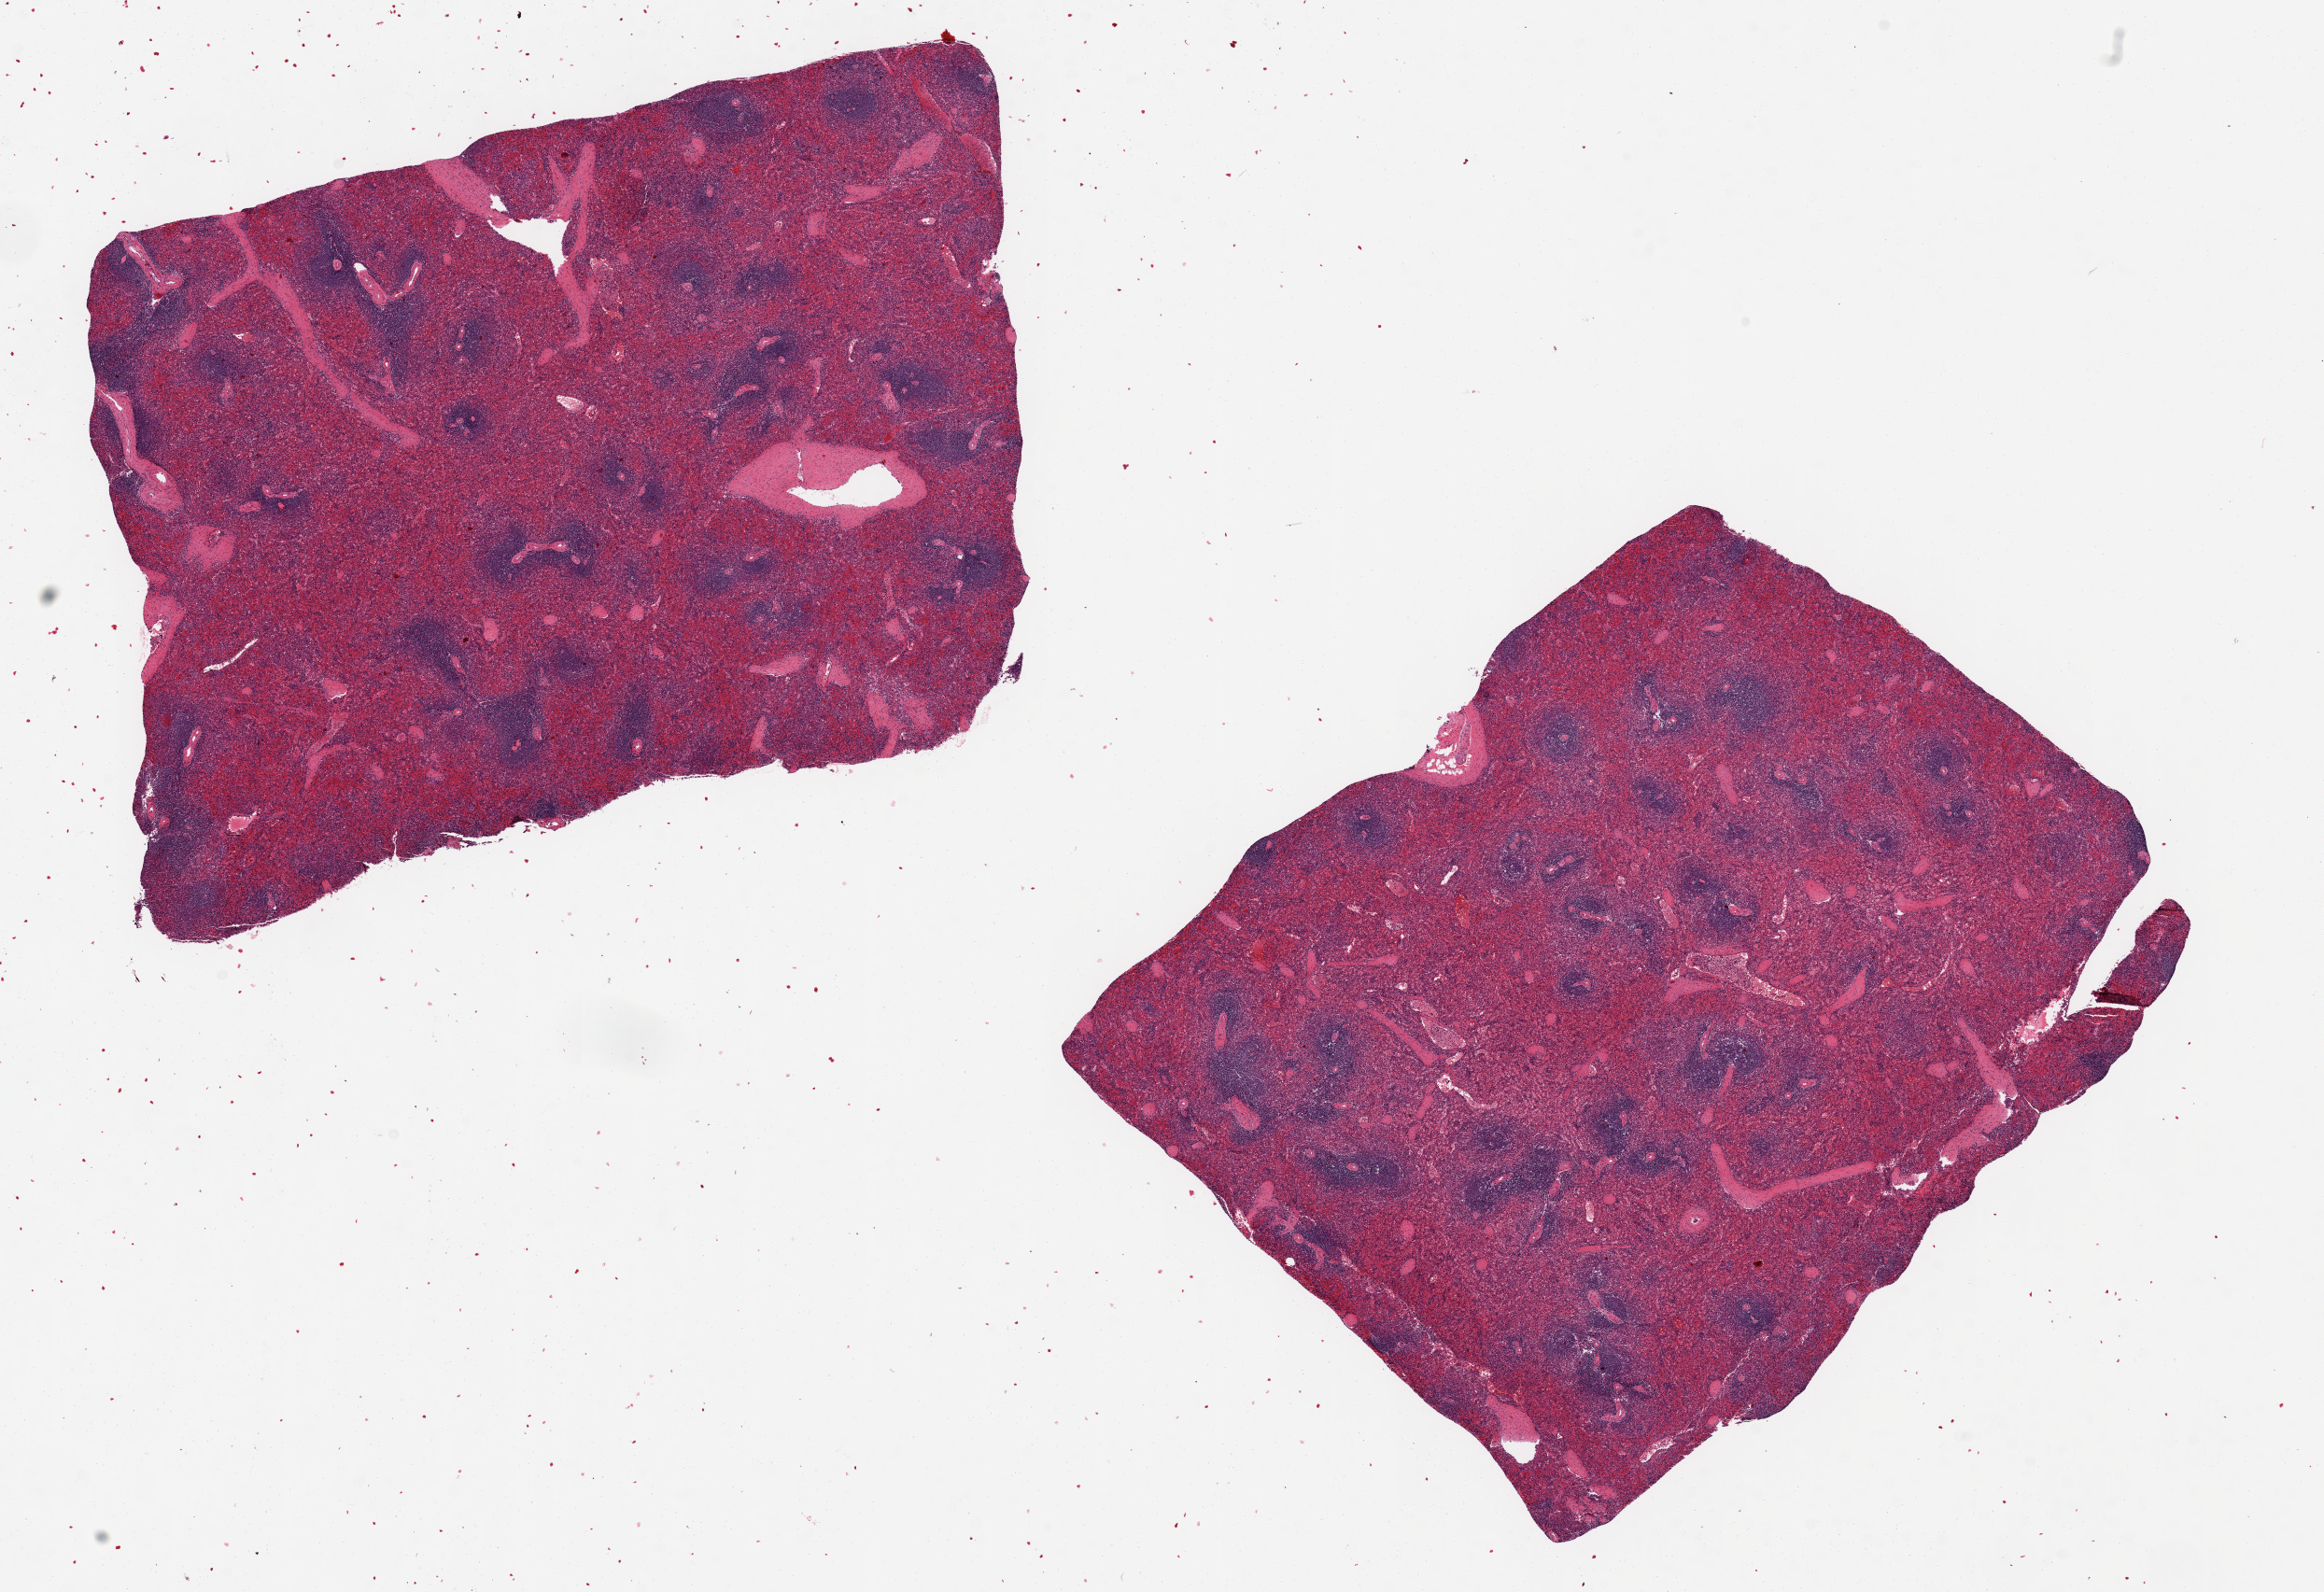
Haematoxylin and eosin whole-slide image — shown as a low-resolution overview of the whole scanned area (about 19.7 x 13.5 mm); PAXgene-fixed paraffin-embedded (PFPE) section; section of spleen (target tissue); tissue donor sample. Donor sex: female.
Pathologist's review note for this sample: 2 aliquots, ~ 7x6mm. Moderate congestion of red pulp.